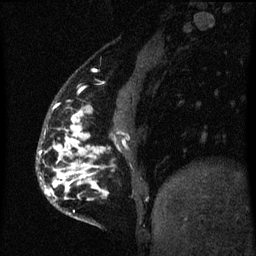
Breast MRI (dynamic contrast-enhanced), one sagittal slice. Position 16 of 60 along the scan axis. Dynamic contrast-enhanced series, image 2 of 3 at this slice position (ordered by acquisition). 1.5 T. TE 4.2 ms, TR 8 ms. 2 mm slice thickness. 256 × 256 image matrix. Female patient, age 50 years.
Annotated regions visible in this slice (semi-automatically segmented with operator editing):
- analysis volume of interest (the breast-tissue region the enhancement analysis was run in; not a lesion): box from (x=40, y=110) to (x=101, y=220) px
- tumour enhancement mask (voxels above the 70 % enhancement threshold inside the analysis volume of interest): (x=40, y=110)–(x=101, y=195)